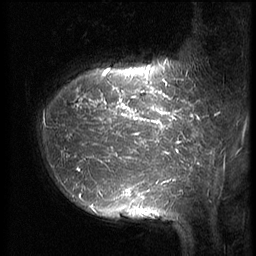
Breast MRI (dynamic contrast-enhanced), one sagittal slice. Slice 14 of 64 in the series (ordered by position). 3 images stored at this slice position (order not interpretable as contrast timing). 1.5 T. TE 4.2 ms, TR 9 ms. 2.5 mm slice thickness. 256 × 256 image matrix. Female patient, age 39 years. From the clinical record (not read from this slice): setting: breast cancer imaged before/during neoadjuvant chemotherapy; receptor status: HER2-positive.
Outlined on this slice (semi-automatic segmentation, software-assisted and operator-edited):
- analysis volume of interest (the breast-tissue region the enhancement analysis was run in; not a lesion): box from (x=36, y=47) to (x=210, y=239) px
- tumour enhancement mask (voxels above the 140 % enhancement threshold inside the analysis volume of interest): (x=64, y=66)–(x=210, y=207)